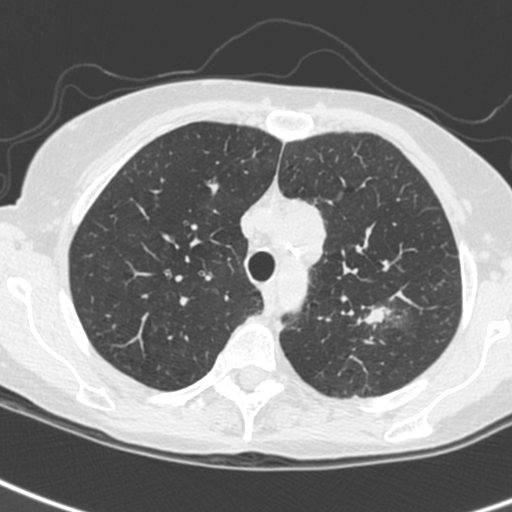
Axial slice from a low-dose chest CT screening exam, baseline annual screen, lung window (W 1500 / L -600 HU), standard (soft-tissue) reconstruction kernel (C), 120 kVp, slice 51 of 242 in the series. Female participant, aged 61 years at enrolment.
Expert reader's lesion annotation, bounding box [x1, y1, x2, y2] px = [344, 291, 411, 346]. The screening reader recorded 2 non-calcified nodules or masses ≥4 mm on this exam (left upper lobe, left upper lobe); which of them this box marks is not recorded. Participant outcome: lung cancer diagnosed 29 days after this screen — small cell carcinoma, NOS, left upper lobe, stage IV (AJCC 6th edition).